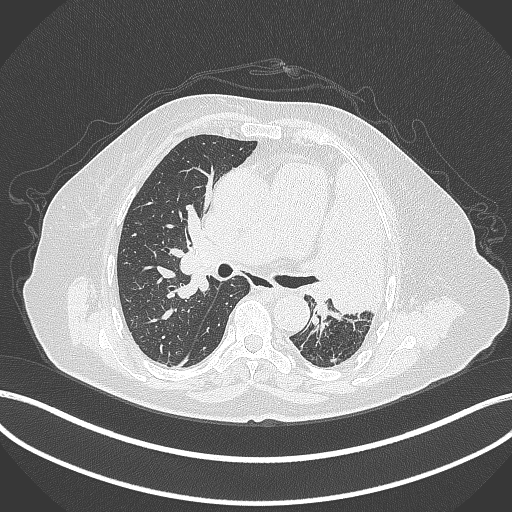
Chest CT, one axial slice. Slice 230 of 399 in the series (ordered by position). Reconstruction kernel B70f. Lung window (W 1500 / L -600 HU). 512 × 512 image matrix. Female patient, age 75 years. From the clinical record (not read from this slice): clinical TNM (as recorded): T3 N3 M1.
Annotated regions visible in this slice (rectangle marked by the reading radiologist):
- lung tumour (recorded histology: adenocarcinoma): bounding box <312,157,395,316> (left, top, right, bottom; pixels)